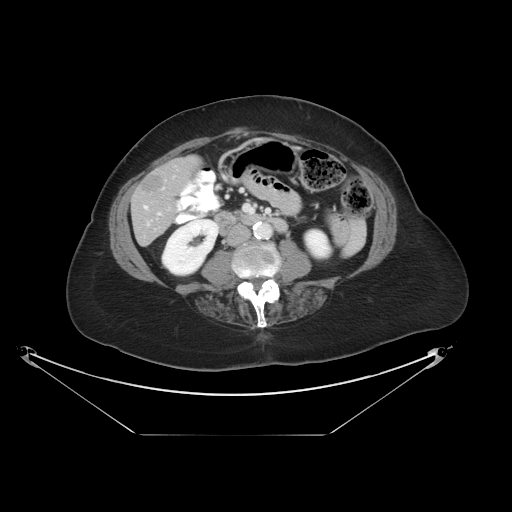
Contrast-enhanced abdominal CT, one axial slice; slice 8 of 36 in the series (ordered by position); 120 kVp; intravenous contrast given; soft-tissue window (W 400 / L 40 HU); 5 mm slice thickness; 512 × 512 image matrix, field of view 500 × 500 mm. Female patient, age 70 years. Case-level facts recorded for this patient, not image findings: diagnosis: colorectal cancer liver metastases, imaged before liver resection; multiple liver metastases: no; largest metastasis: 2.5 cm; disease in both lobes: no.
Outlined on this slice (expert manual segmentation):
- hepatic veins: bounding box (x1, y1, x2, y2) in pixels: (144, 206, 147, 209)
- liver: (133, 159, 198, 245)
- planned liver remnant (the part of the liver to remain after resection): (177, 158, 198, 179)
- liver metastasis: (143, 174, 162, 195)